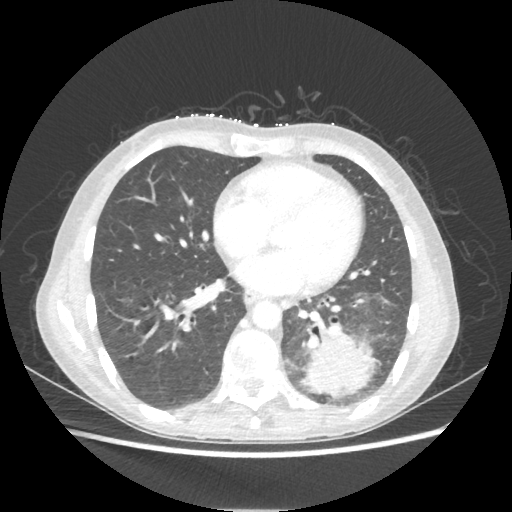
Chest CT, one axial slice; slice 90 of 221 in the series (ordered by position); reconstruction kernel STANDARD; 80 kVp; lung window (W 1500 / L -600 HU); 1.25 mm slice thickness; 512 × 512 image matrix, field of view 360 × 360 mm. Patient: female, 53 years. From the clinical record (not read from this slice): clinical TNM (as recorded): T3 N0 M0.
Outlined on this slice (rectangle marked by the reading radiologist):
- lung tumour (recorded histology: adenocarcinoma): bounding box <298,329,377,397> (left, top, right, bottom; pixels)